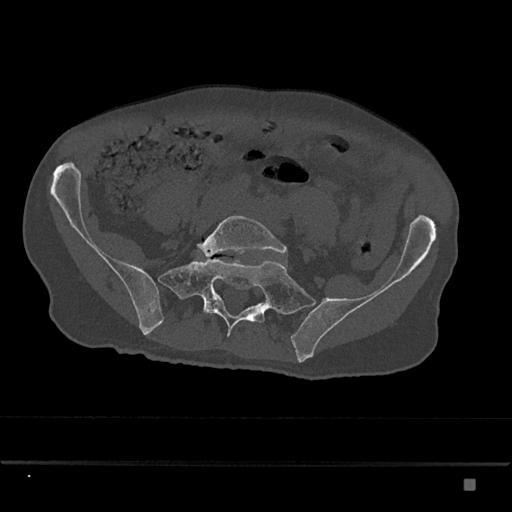
CT including the spine, one axial slice; slice 236 of 797 in the series (ordered by position); 120 kVp; bone window (W 1800 / L 400 HU); 0.5 mm slice thickness; 512 × 512 image matrix, field of view 390 × 390 mm. Patient: male, 72 years. From the clinical record (not read from this slice): primary cancer: prostate.
Annotated regions visible in this slice (semi-automatically segmented with operator editing):
- L5 vertebra: box from (x=198, y=216) to (x=288, y=257) px